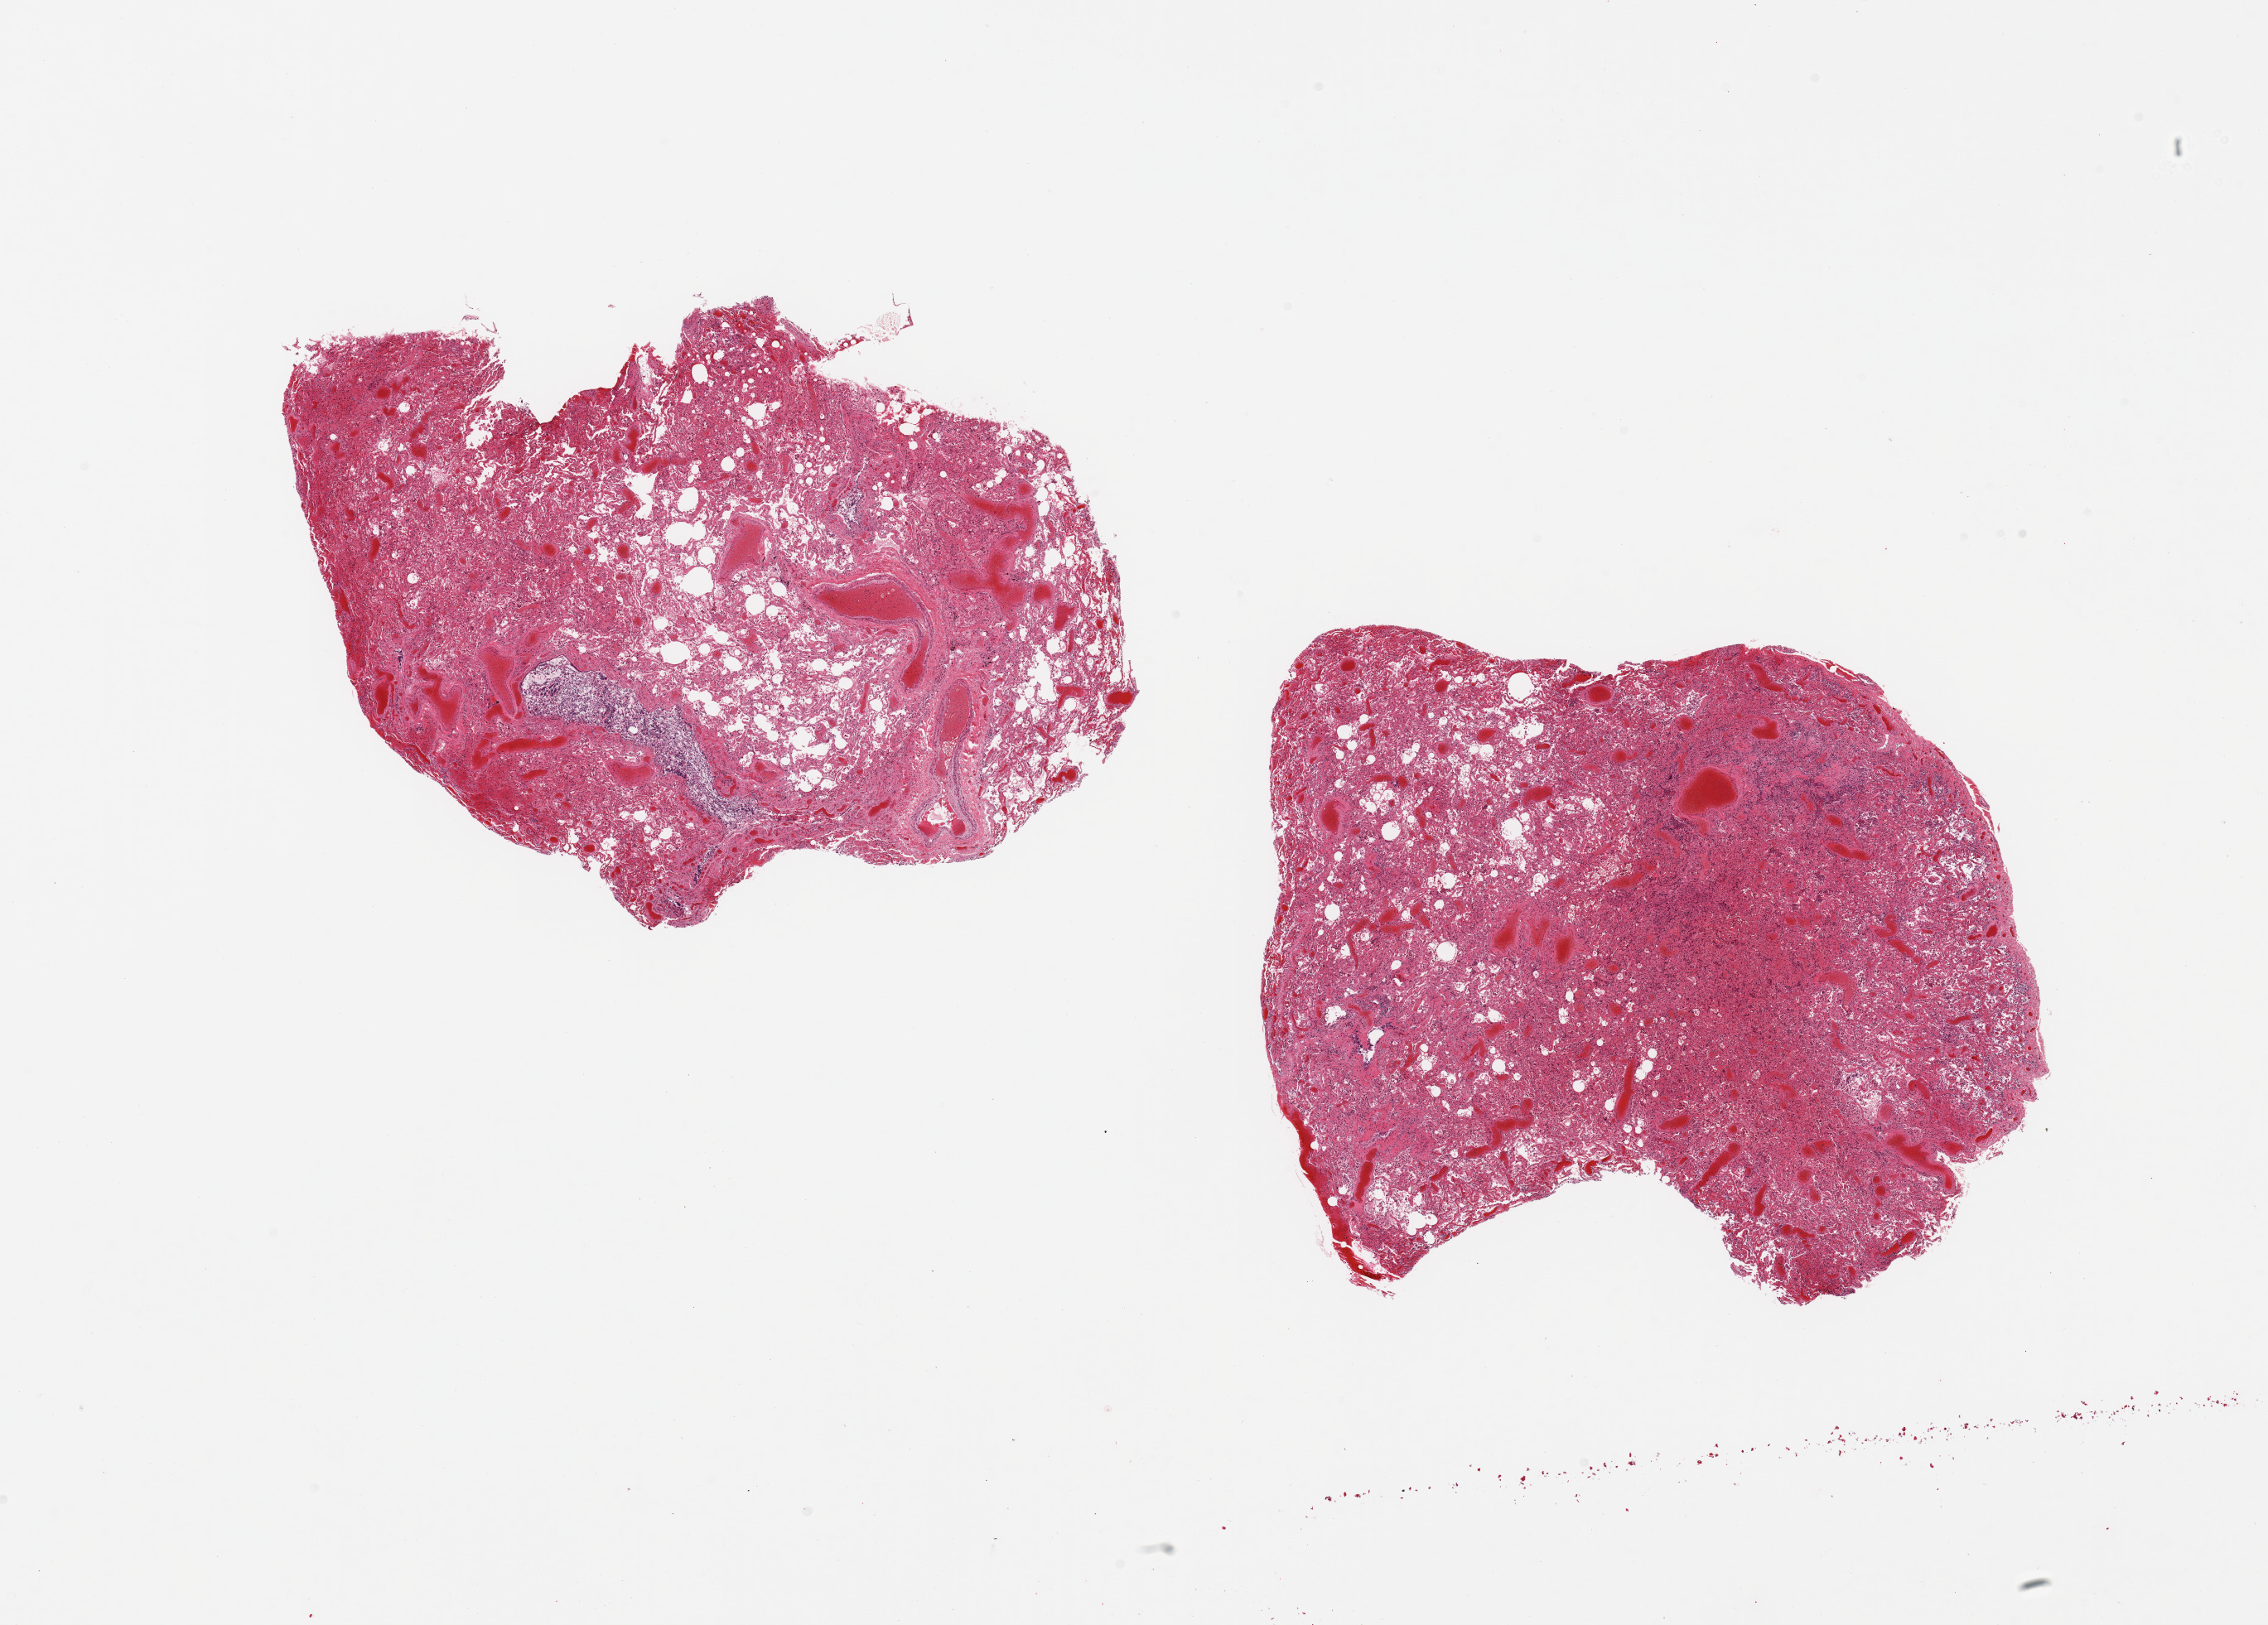
Haematoxylin and eosin whole-slide image, a low-resolution overview of the entire scanned area, about 21.7 x 15.5 mm. PAXgene-fixed paraffin-embedded (PFPE) section. Section of lung (target tissue). Donor tissue sample. Donor sex: male.
Reviewer comment on this tissue sample: 2 pieces; severe vascular congestion with fibrosis consistent with heart failure.